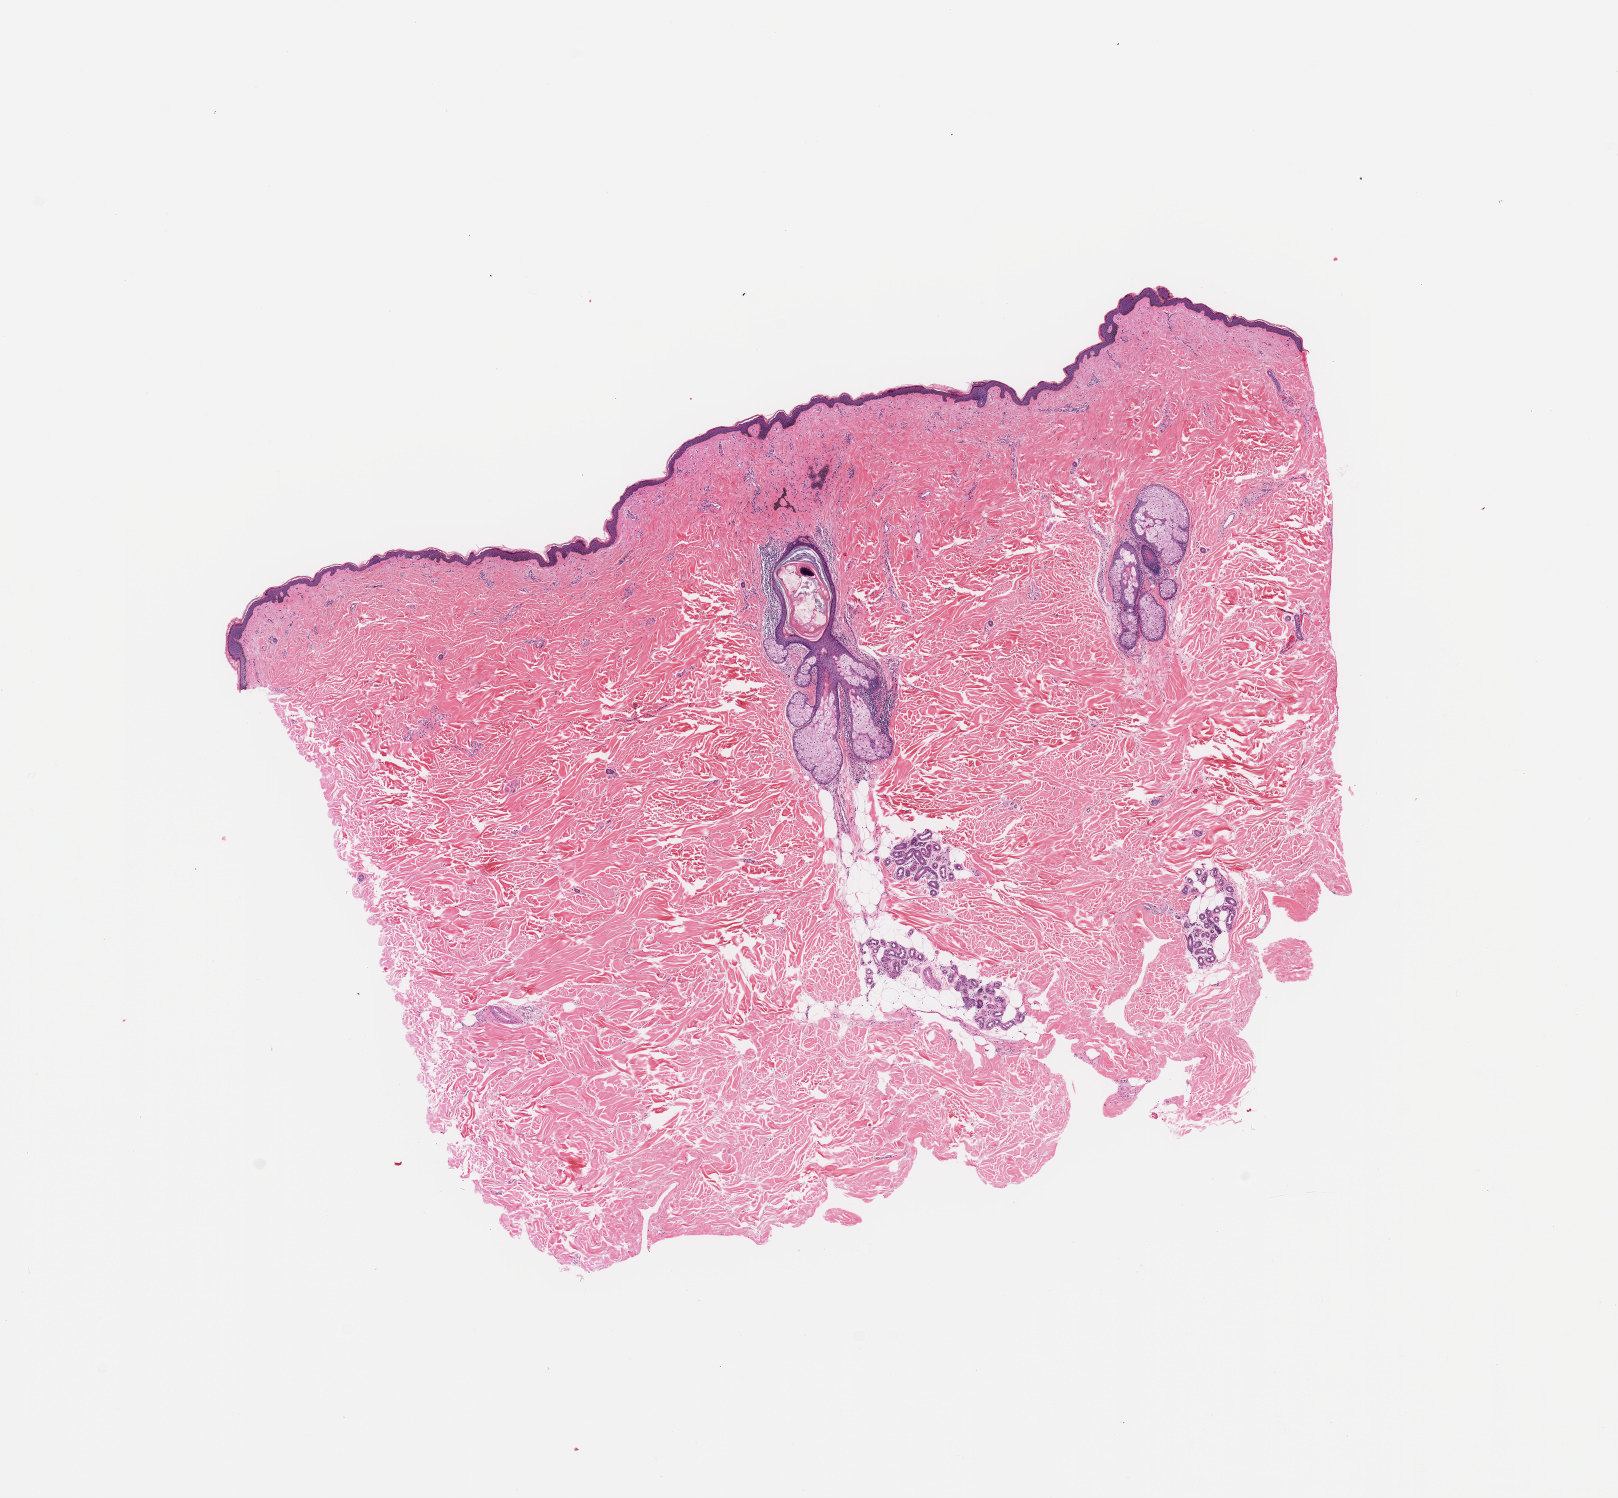
Whole-slide histology image, H&E — low-resolution overview of the scanned area, about 12.8 x 11.8 mm (acquisition: 20x scan); normal (non-tumour) tissue sample, sampled site: trunk. 78-year-old male patient.
- this section: normal (non-tumour) tissue from the same patient
- patient diagnosis: Malignant melanoma, NOS